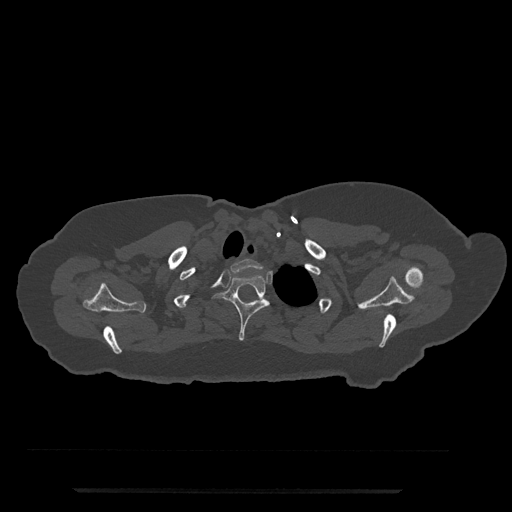
CT including the spine, one axial slice. Slice 675 of 797 in the series (ordered by position). Bone window (W 1800 / L 400 HU). 0.5 mm slice thickness. 512 × 512 image matrix, field of view 440 × 440 mm. Patient: female, 51 years. From the clinical record (not read from this slice): primary cancer: neuro; vertebrae with lytic lesions (as recorded): T8.
Structures marked on this image (semi-automatic segmentation, software-assisted and operator-edited):
- T1 vertebra: bounding box (x1, y1, x2, y2) in pixels: (231, 259, 262, 273)
- T2 vertebra: (214, 274, 270, 341)